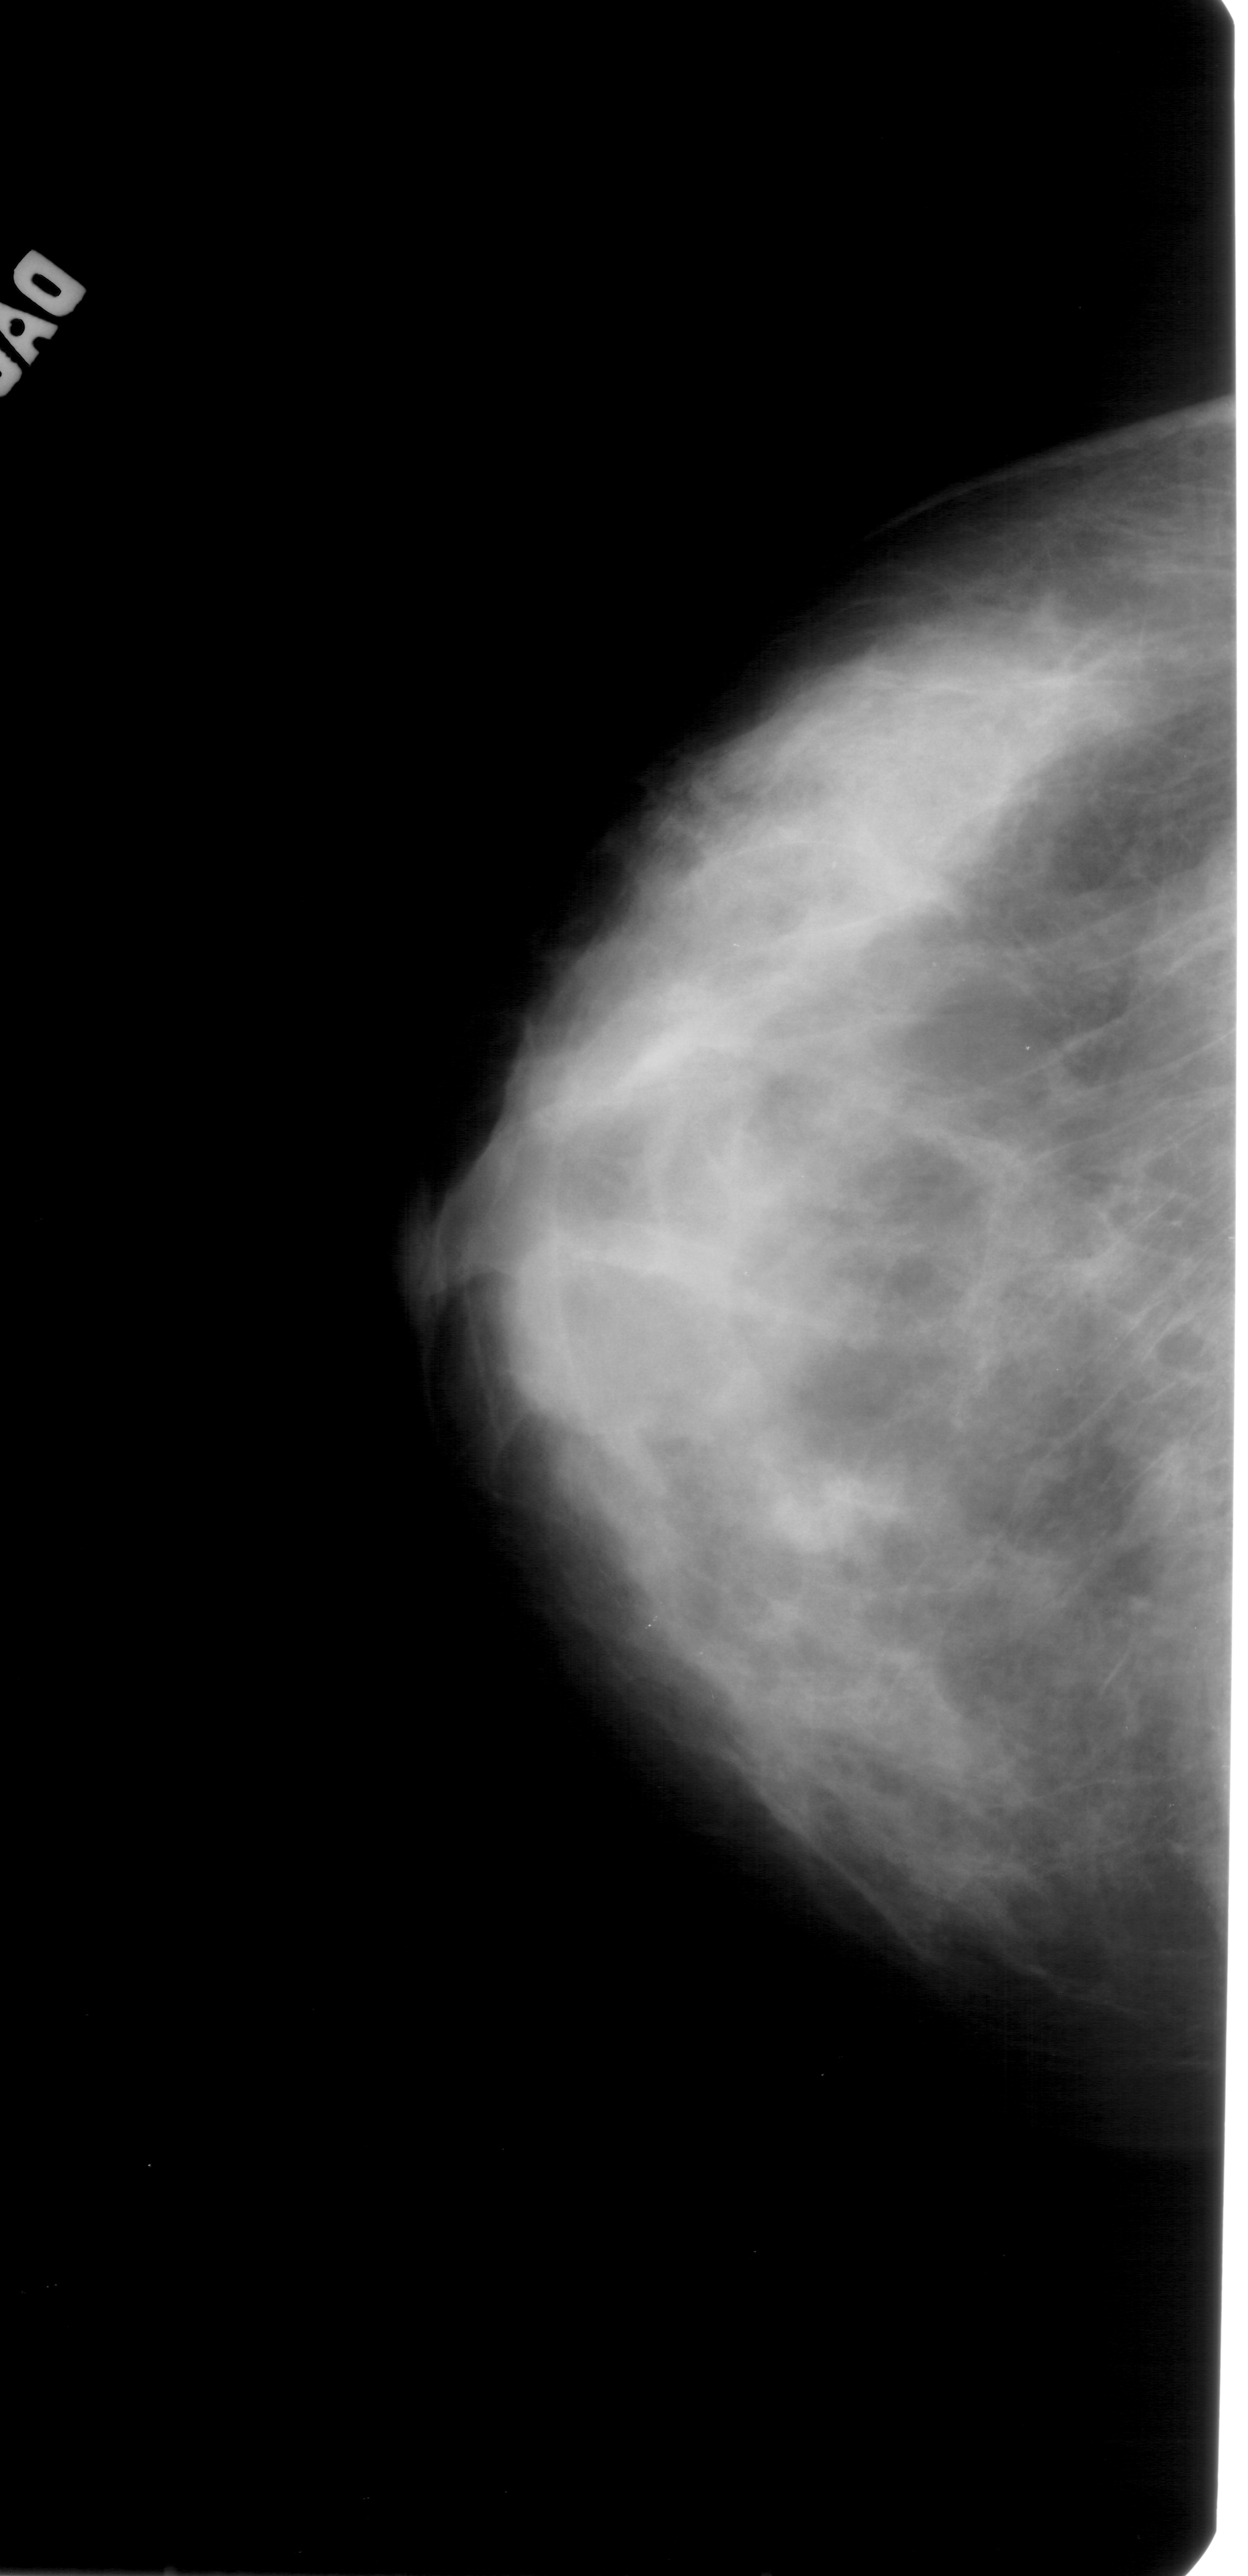
Mammogram (digitized film); left breast; craniocaudal (CC) view; 1248 × 2576 image matrix.
Expert-marked regions of interest on this film, with their recorded descriptors:
- calcifications, morphology pleomorphic, distribution segmental; BI-RADS assessment category 4; pathology (as recorded): benign: box from (x=690, y=814) to (x=999, y=994) px